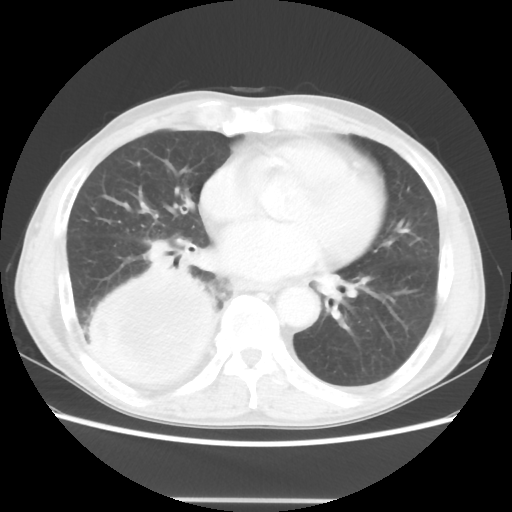
Chest CT, one axial slice. Slice 18 of 48 in the series (ordered by position). 100 kVp. Lung window (W 1500 / L -600 HU). 512 × 512 image matrix, field of view 361 × 361 mm. Patient: male, 66 years. Case-level facts recorded for this patient, not image findings: clinical TNM (as recorded): T4 N1 M1; histopathological grade: G3.
Annotated regions visible in this slice (rectangle marked by the reading radiologist):
- lung tumour (recorded histology: small cell carcinoma): bounding box <81,263,222,396> (left, top, right, bottom; pixels)